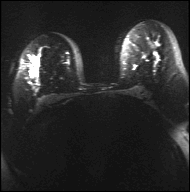
Breast MRI, one axial slice. Diffusion-weighted series; image 2 of 4 stored at this slice position (different b-values; order by instance number). 3 T. 4 mm slice thickness. 190 × 192 image matrix. Female patient.
Structures marked on this image (expert manual segmentation):
- tumour on diffusion-weighted imaging: bounding box <81,68,89,72> (left, top, right, bottom; pixels)